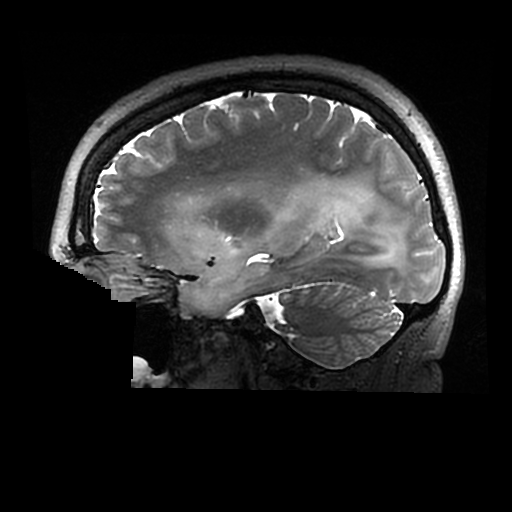
Brain MRI from a brain-tumour surgery series, one sagittal slice. Position 192 of 320 along the scan axis. 0.6 mm slice thickness. 512 × 512 image matrix, field of view 240 × 240 mm. From the clinical record (not read from this slice): histopathology: Astrocytoma; WHO grade: 2; IDH mutation: yes.
Annotated regions visible in this slice (expert manual segmentation):
- tumour: box from (x=177, y=184) to (x=406, y=314) px